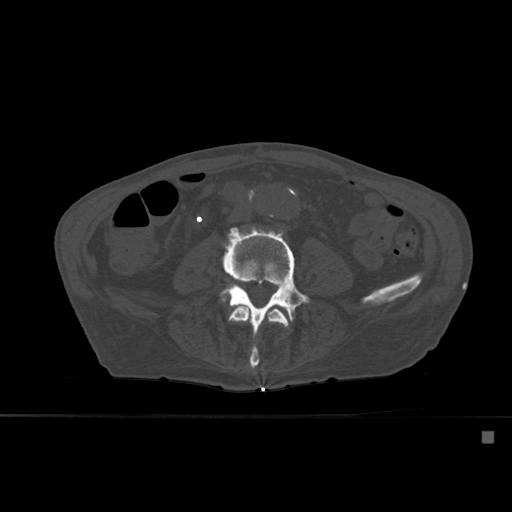
CT including the spine, one axial slice; slice 196 of 527 in the series (ordered by position); bone window (W 1800 / L 400 HU); 1.5 mm slice thickness; 512 × 512 image matrix, field of view 373 × 373 mm. Patient: male, 78 years. Case-level facts recorded for this patient, not image findings: primary cancer: prostate.
Annotated regions visible in this slice (semi-automatic segmentation, software-assisted and operator-edited):
- L3 vertebra: bounding box (x1, y1, x2, y2) in pixels: (228, 306, 289, 371)
- L4 vertebra: (219, 227, 311, 350)